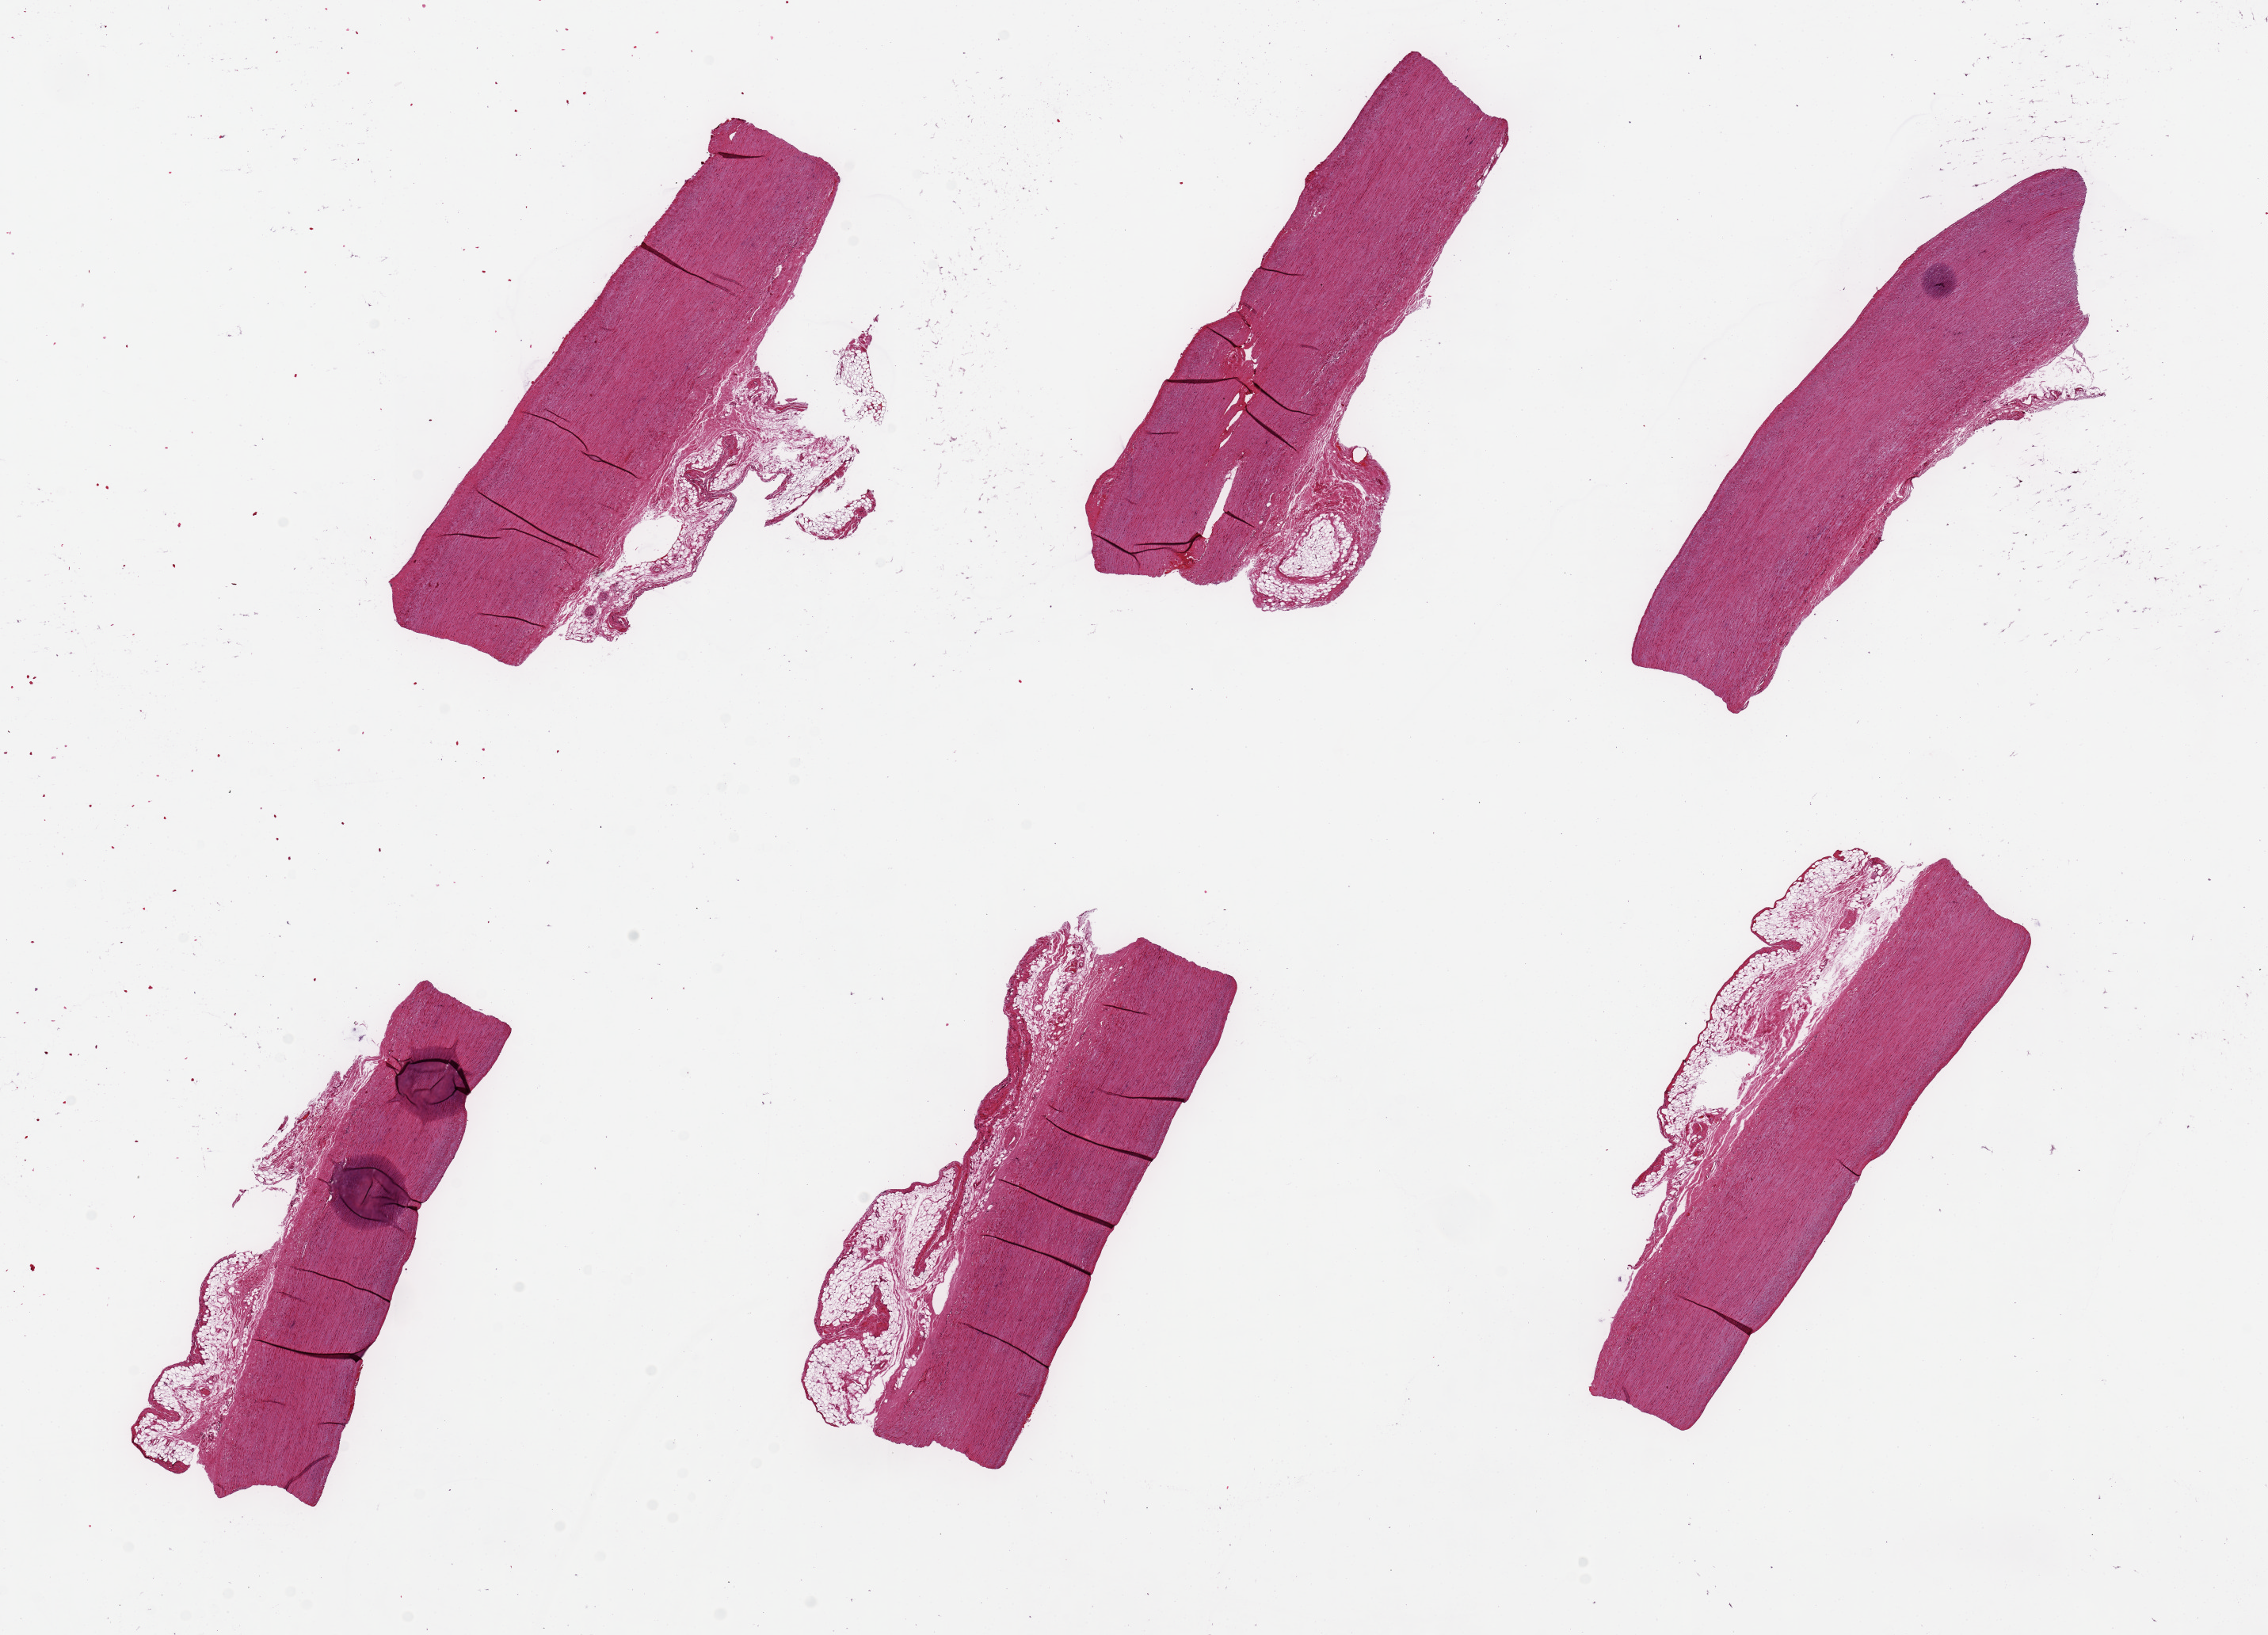
Whole-slide image, haematoxylin and eosin stain — whole scanned area (about 22.6 x 16.3 mm, slide scanned at 20x) shown as a low-resolution overview; PAXgene-fixed paraffin-embedded (PFPE) section; section of aorta (target tissue); donor tissue sample. Male donor.
Reviewer comment on this tissue sample: 6 pieces, up to 6.5x2mm; up to 1 mm peripheral adipose.